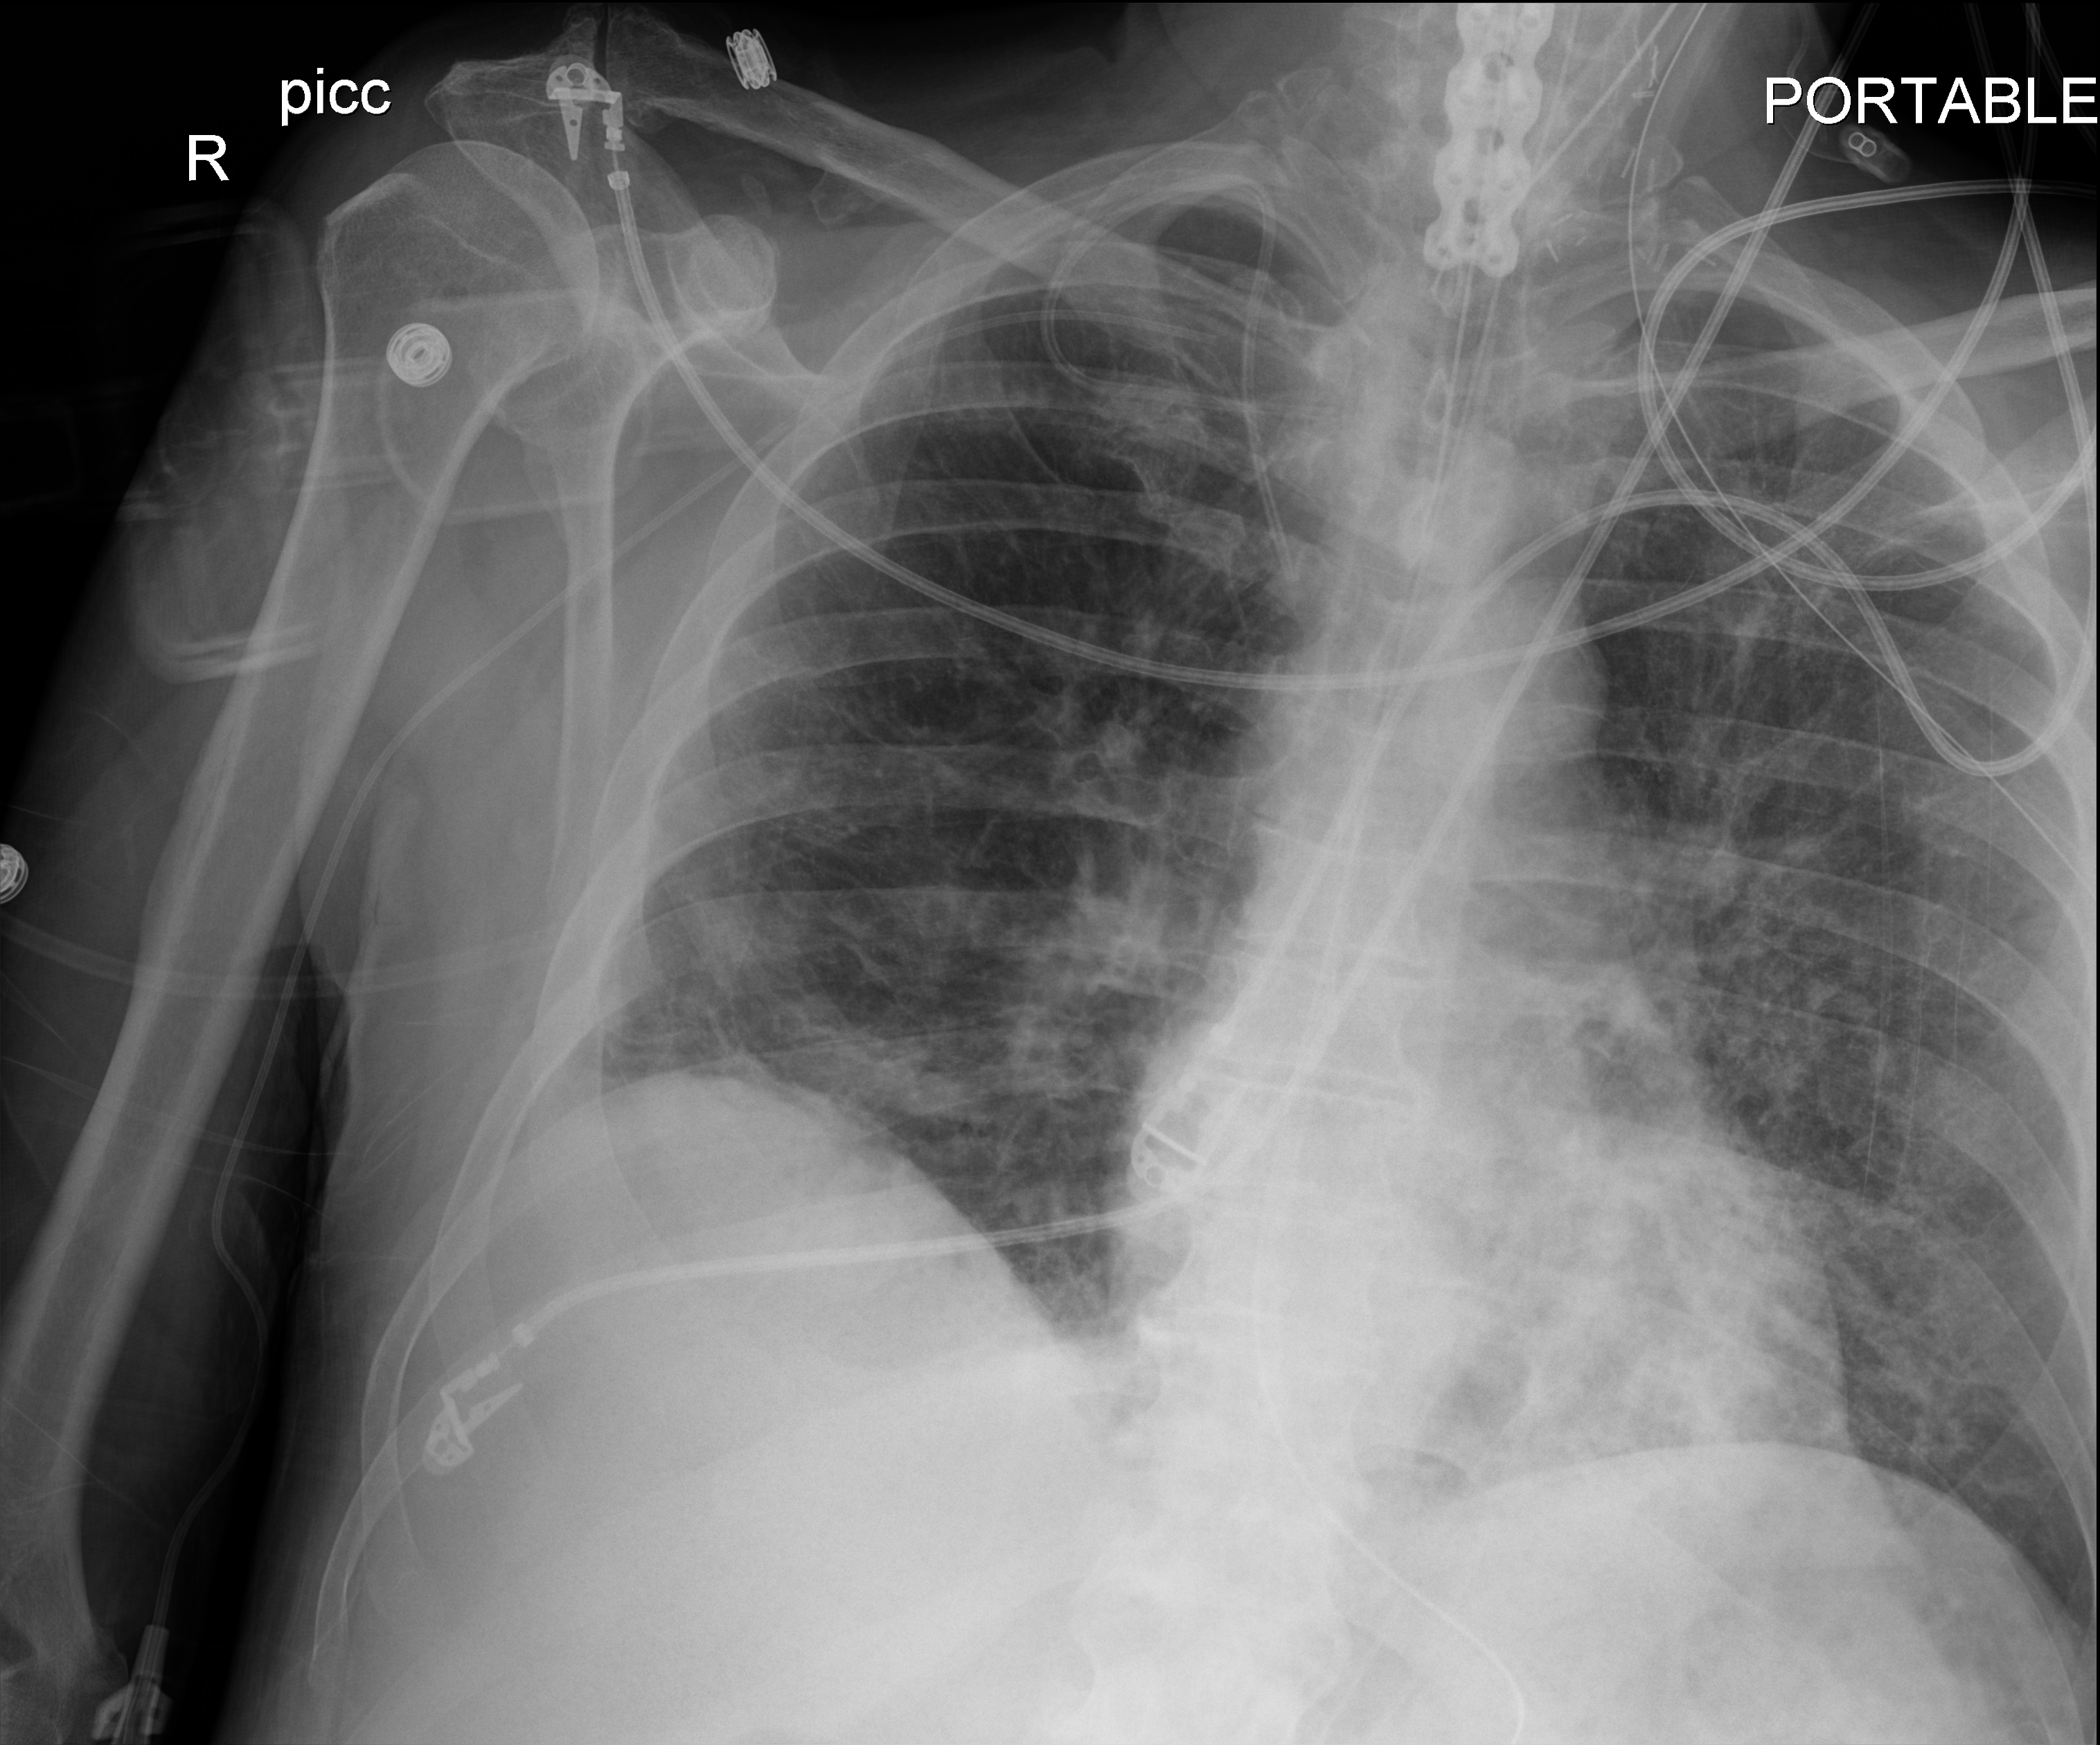
Chest X-ray (portable), anteroposterior (AP) projection. Patient hospitalised with COVID-19; male, aged 60–74 years.
Hospital-stay facts (about this admission, not read from this image; timing relative to this image not recorded):
- mechanically ventilated during this hospital stay: yes